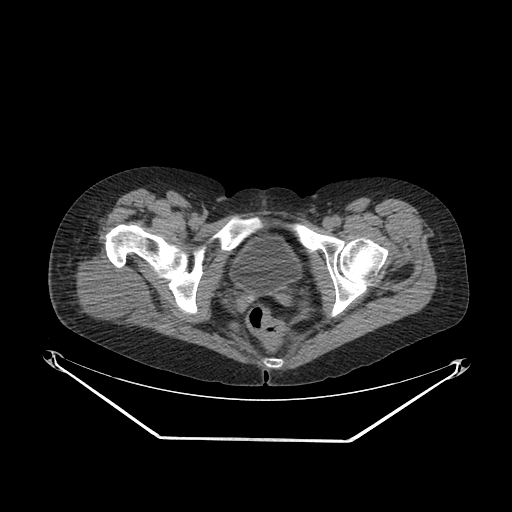
CT of an extremity soft-tissue mass (from a PET/CT study), one axial slice; position 46 of 267 along the scan axis; reconstruction kernel SOFT; 140 kVp; soft-tissue window (W 400 / L 40 HU); 512 × 512 image matrix, field of view 500 × 500 mm. Female patient. From the clinical record (not read from this slice): histological type: epithelioid sarcoma with vascular differentiation; site of the primary tumour: right buttock.
Structures marked on this image (expert contour drawn on MRI and transferred to this co-registered scan by the dataset authors):
- gross tumour volume (mass): bounding box <66,253,152,332> (left, top, right, bottom; pixels)